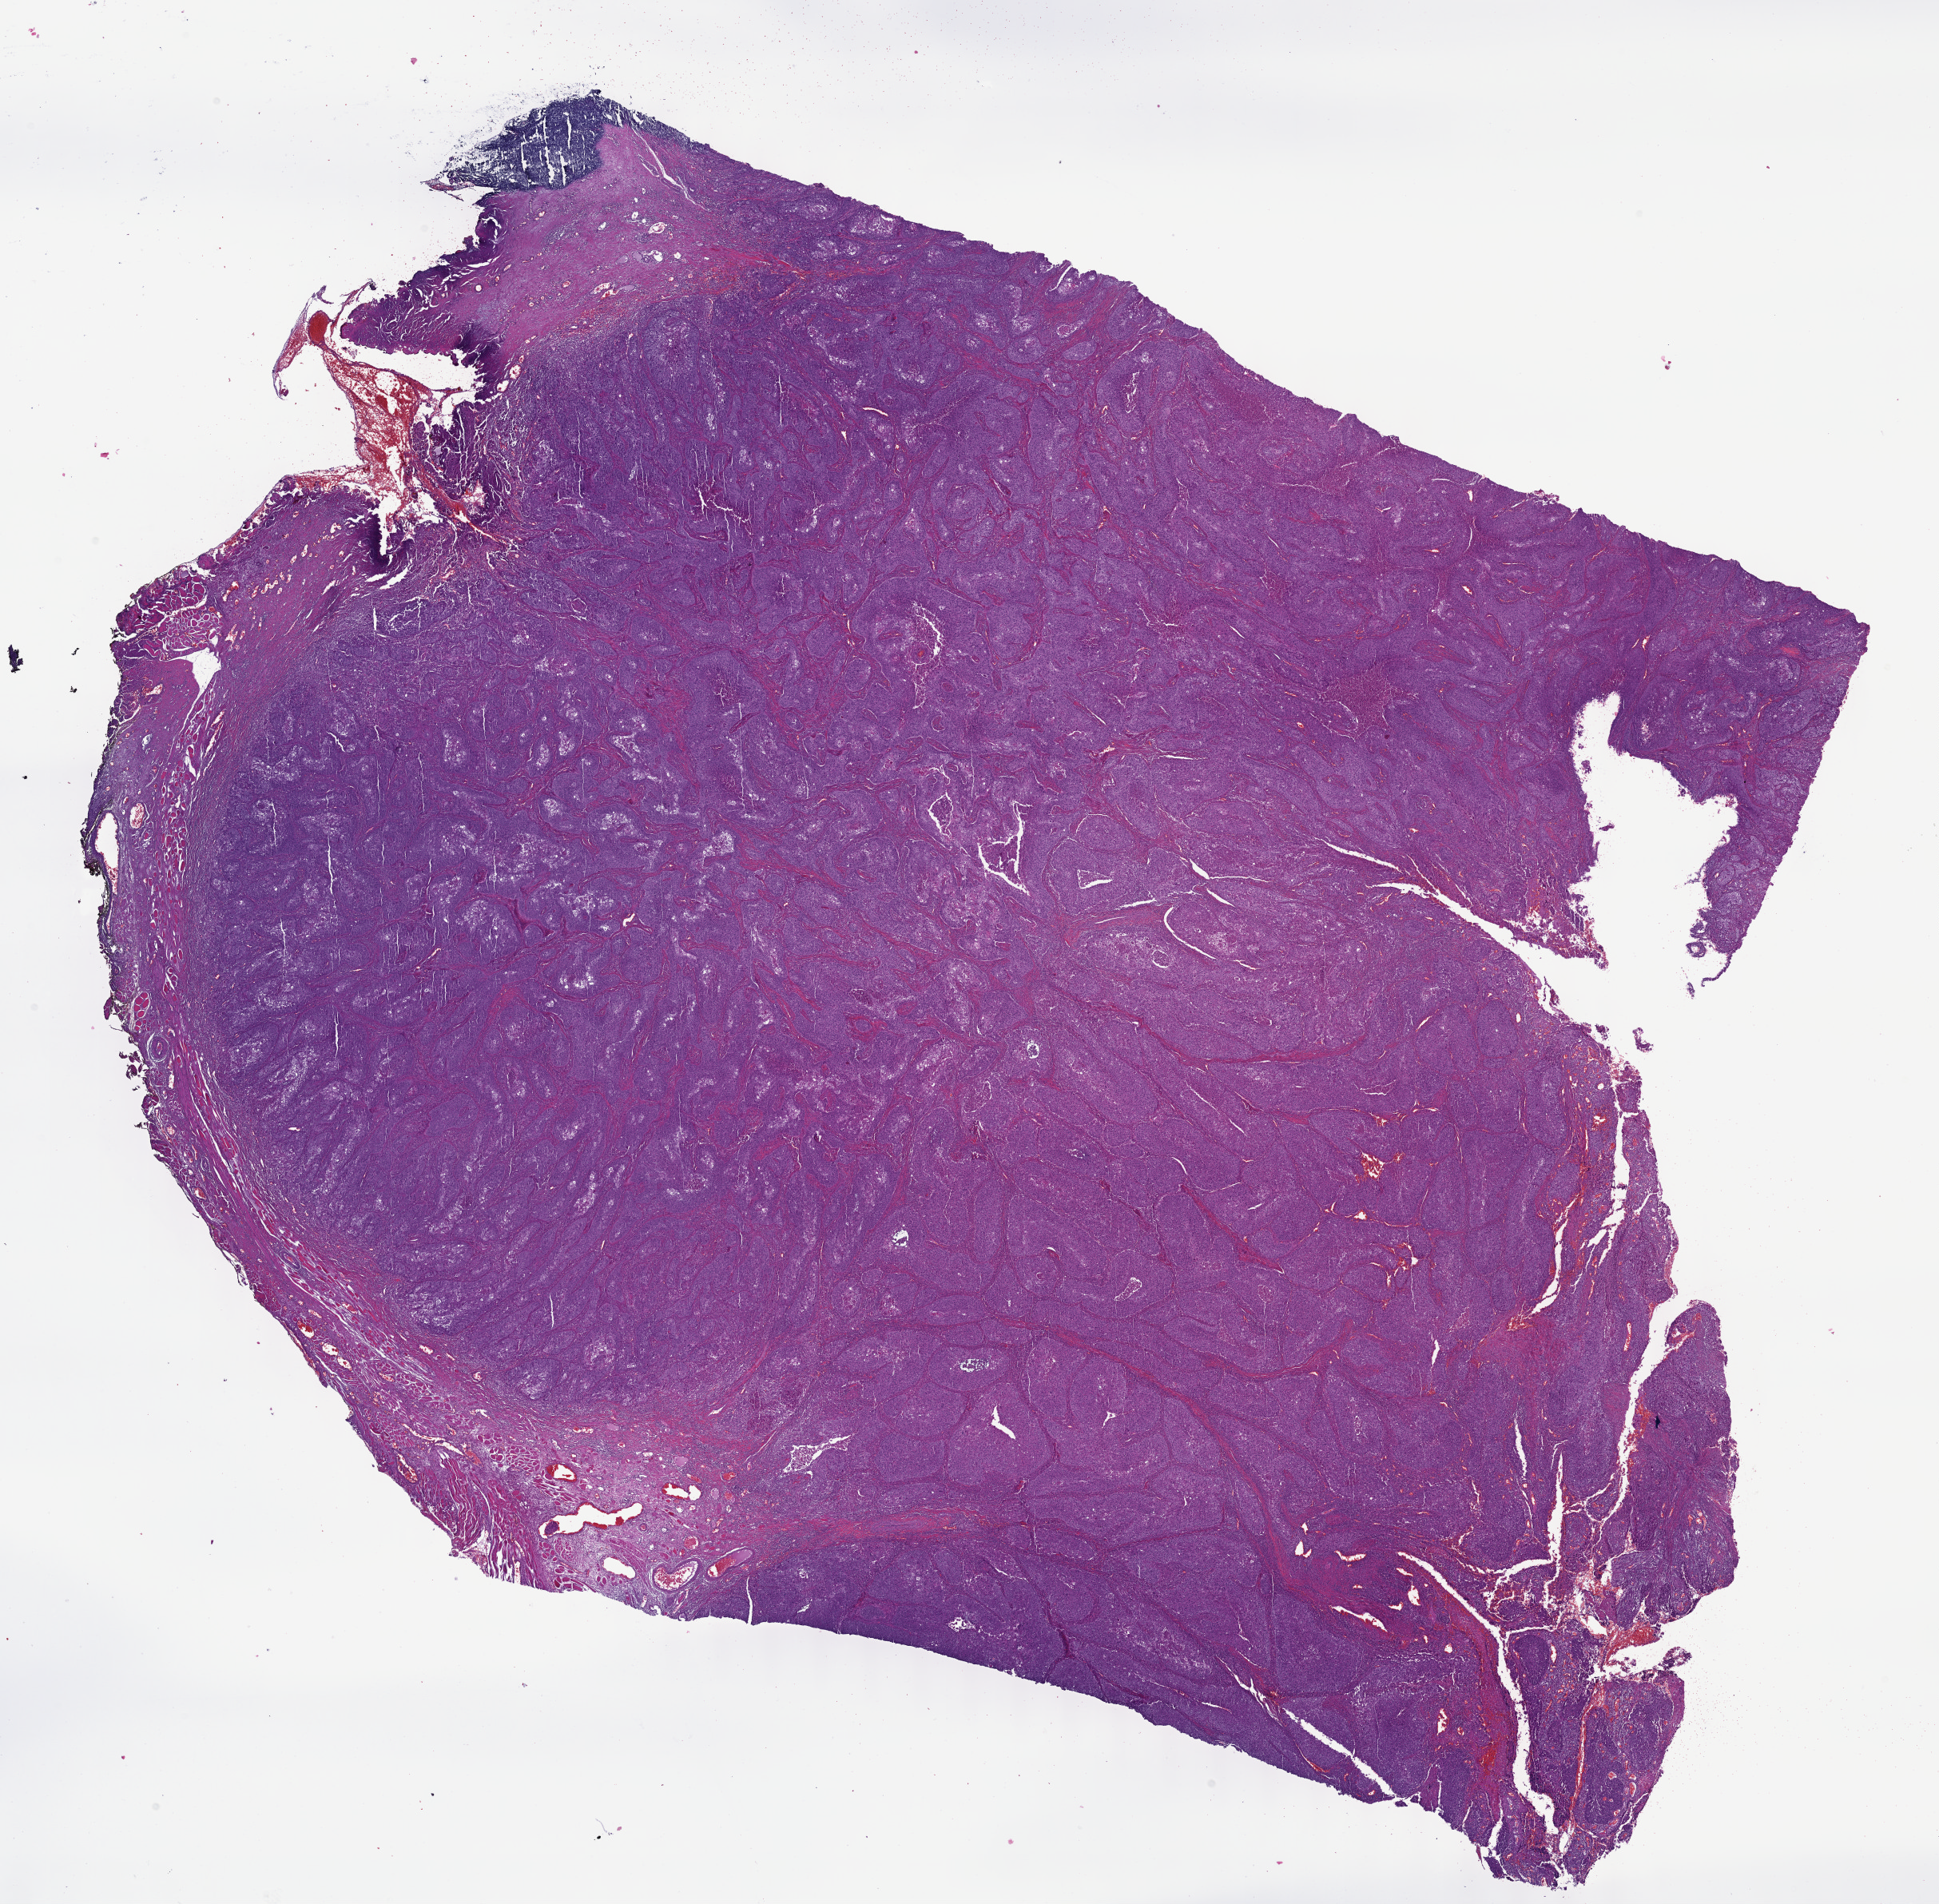
Digitized H&E tissue section (whole slide), whole scanned area (about 19.6 x 19.3 mm, acquisition: 40x scan) shown as a low-resolution overview, formalin-fixed paraffin-embedded (FFPE) diagnostic section, sample: primary tumour, head and neck. Patient: male, age at initial diagnosis 43 years. Histologic grade: G3 (poorly differentiated).
Histologic diagnosis: Squamous cell carcinoma, NOS. AJCC pathologic stage: IVB (7th edition).